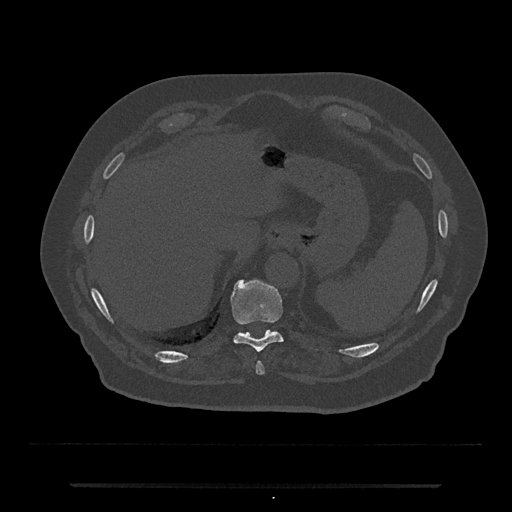
CT including the spine, one axial slice. 120 kVp. Bone window (W 1800 / L 400 HU). 512 × 512 image matrix. Patient: male, 80 years. Case-level facts recorded for this patient, not image findings: primary cancer: prostate.
Outlined on this slice (semi-automatic segmentation, software-assisted and operator-edited):
- T10 vertebra: box from (x=230, y=279) to (x=283, y=352) px
- T11 vertebra: (x=271, y=330)–(x=276, y=332)
- T9 vertebra: (x=256, y=362)–(x=265, y=375)